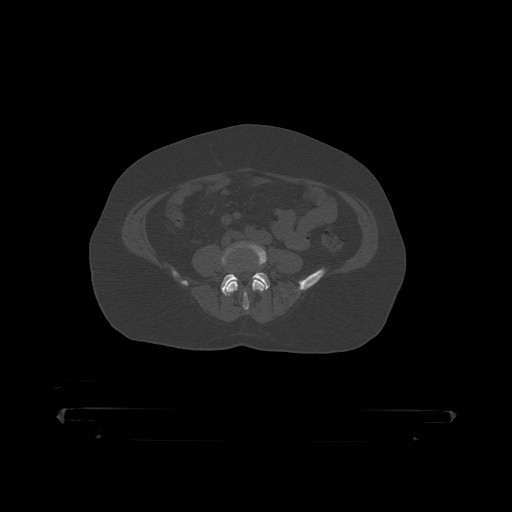
CT including the spine, one axial slice; position 52 of 390 along the scan axis; reconstruction kernel STANDARD; 120 kVp; bone window (W 1800 / L 400 HU); 1.25 mm slice thickness; 512 × 512 image matrix. Male patient, age 60 years. Case-level facts recorded for this patient, not image findings: primary cancer: prostate.
Annotated regions visible in this slice (semi-automatically segmented with operator editing):
- L4 vertebra: bounding box (x1, y1, x2, y2) in pixels: (222, 241, 267, 311)
- L5 vertebra: (221, 269, 270, 296)